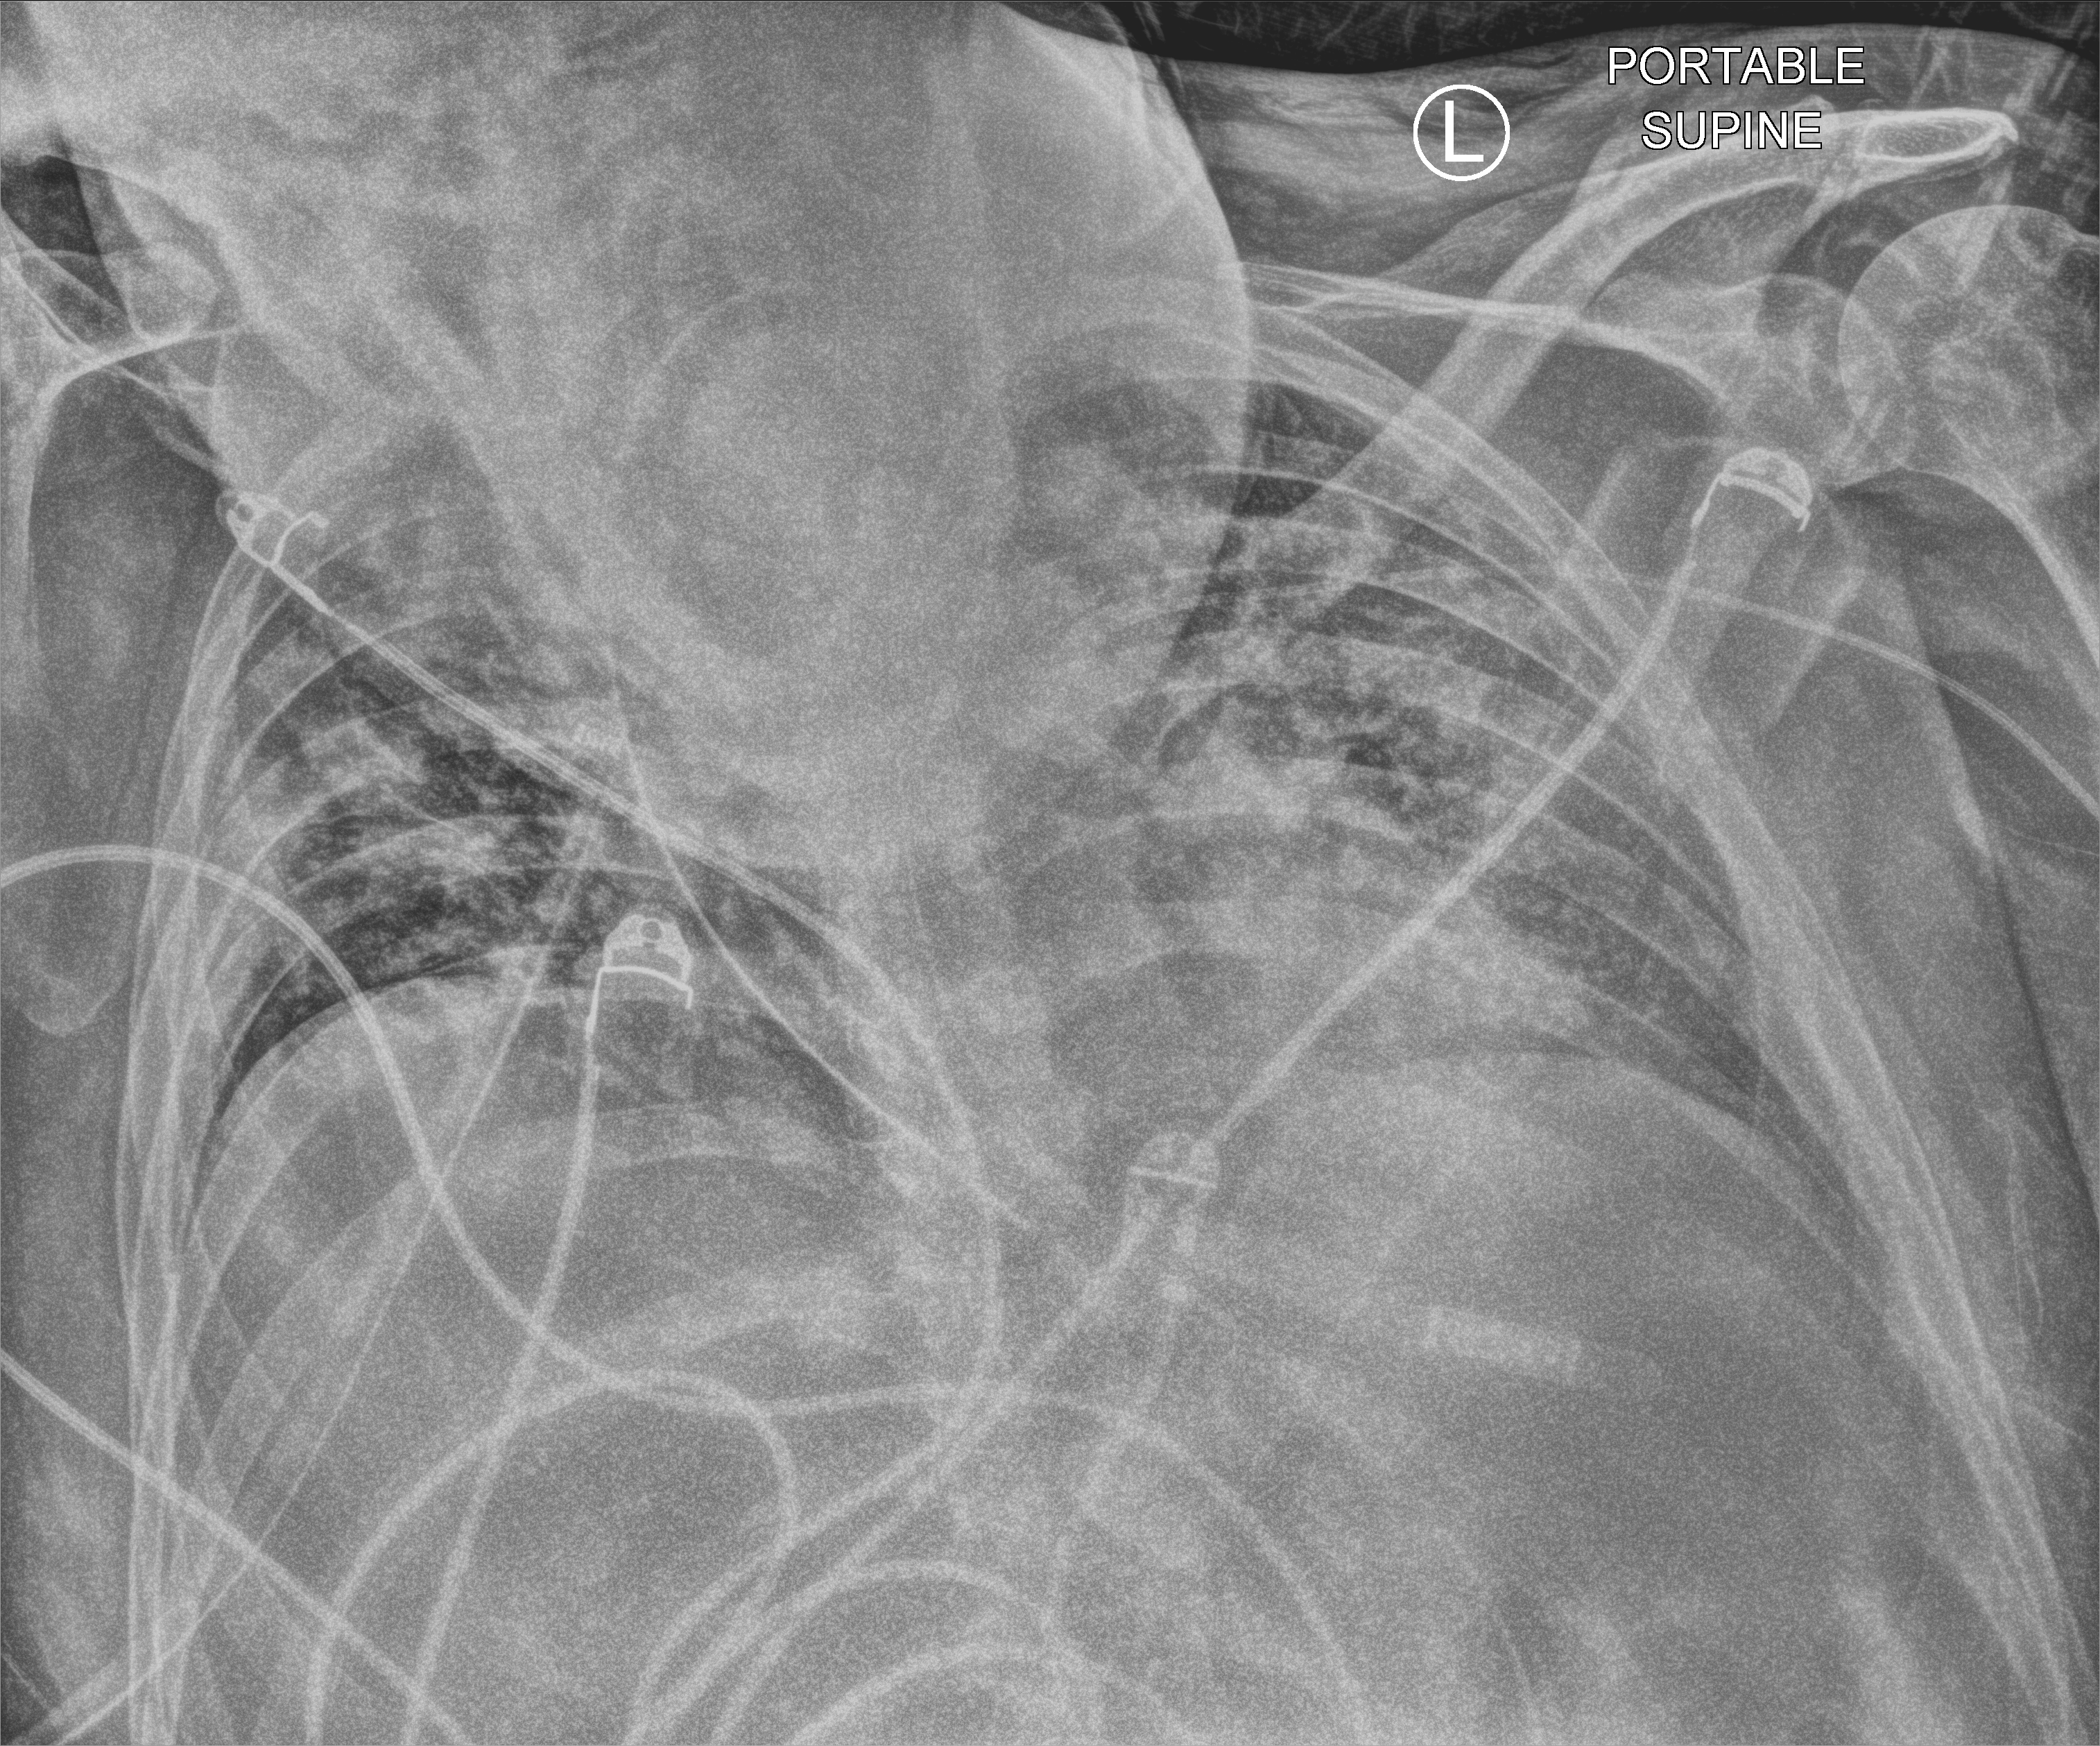
Chest X-ray (portable); anteroposterior (AP) projection. Patient hospitalised with COVID-19; male, aged 18–59 years.
From the hospital-stay record, not from the radiograph (when in the stay this image was taken is not recorded):
- COPD (admission record): no
- mechanically ventilated during this hospital stay: yes
- admitted to intensive care during this hospital stay: yes